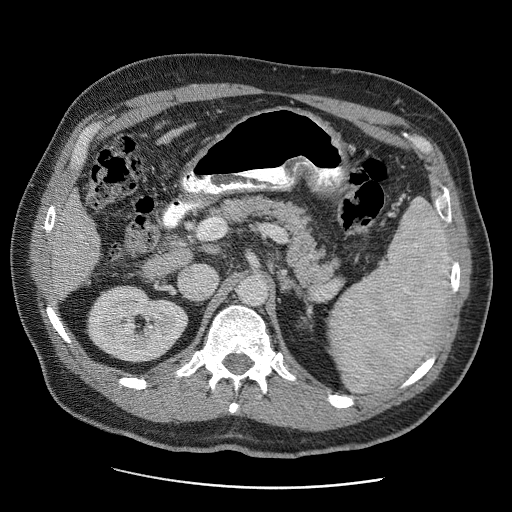
Contrast-enhanced abdominal CT (liver protocol), one axial slice. Position 17 of 81 along the scan axis. Reconstruction kernel STANDARD. 120 kVp. Soft-tissue window (W 400 / L 40 HU). 2.5 mm slice thickness. 512 × 512 image matrix, field of view 380 × 380 mm. From the clinical record (not read from this slice): diagnosis: hepatocellular carcinoma (patient treated with transarterial chemoembolisation; whether this scan precedes or follows treatment is not stated here); TNM stage (as recorded): Stage-IIIA; Child-Pugh class: A; tumour nodularity: multinodular; tumour size: 5.5 cm.
Outlined on this slice (semi-automatically segmented with operator editing):
- liver parenchyma outside the tumour (the mass and vessels are separate outlines, so this box may not span the whole liver): bounding box [x1, y1, x2, y2] px = [44, 193, 100, 297]